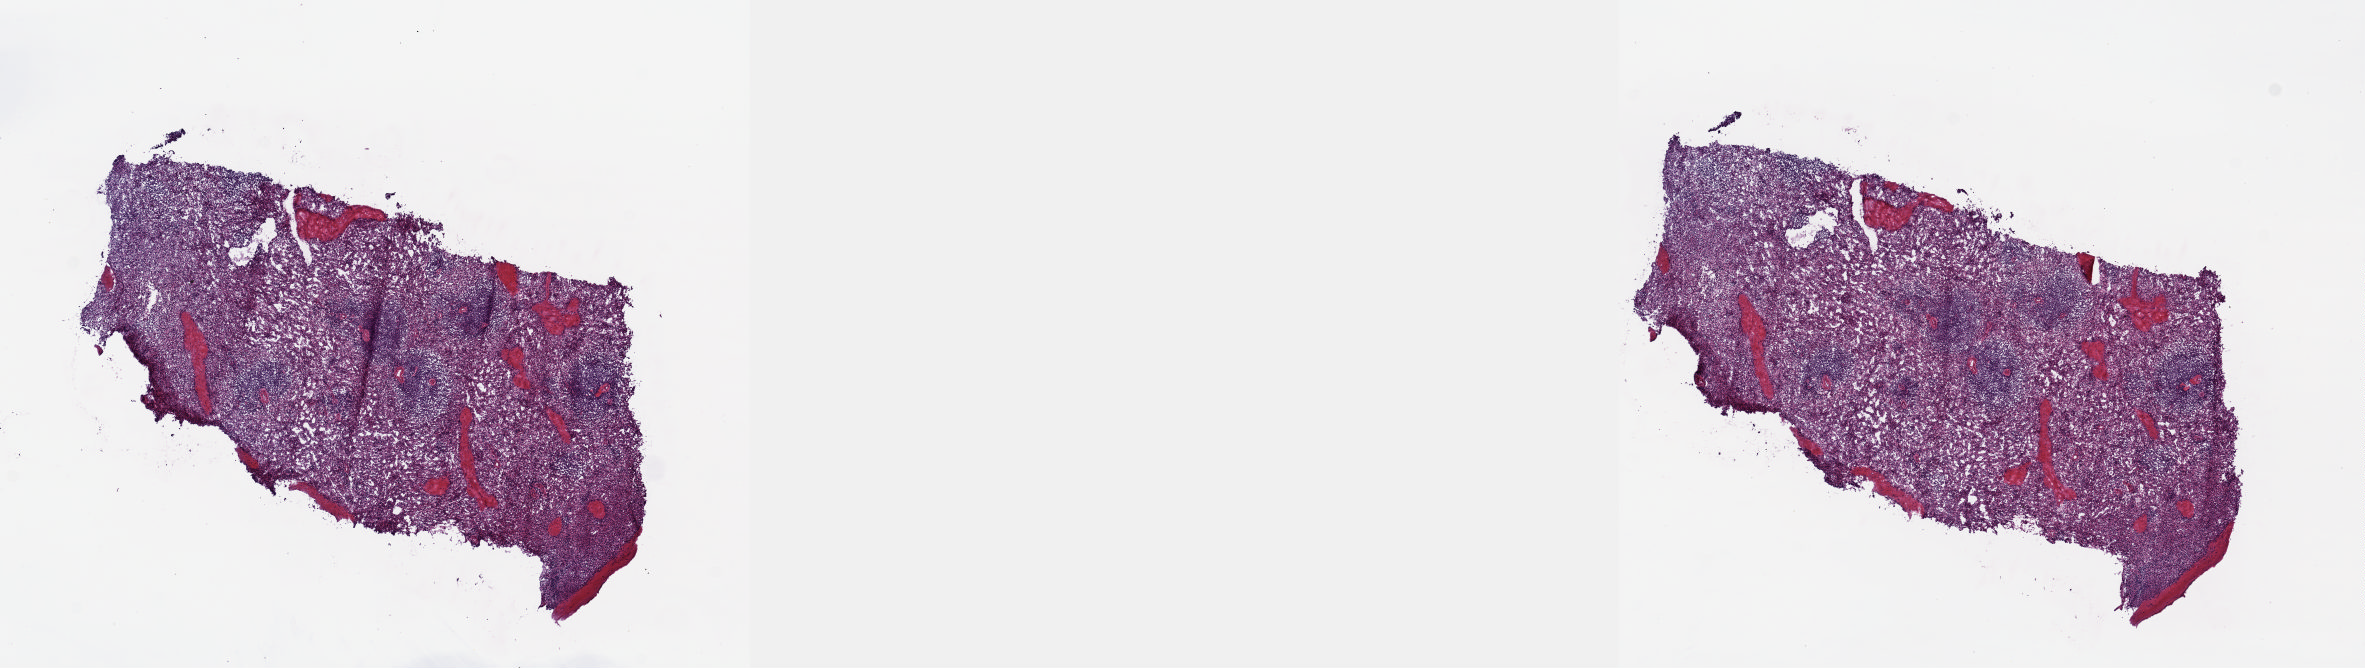
Digitized H&E tissue section (whole slide) — shown as a low-resolution overview of the whole scanned area (about 19.1 x 5.4 mm, slide scanned at 20x). Frozen section from the top of the tissue portion. Sample: solid tissue normal (non-tumour tissue), pancreas. Male, age 85 years at initial diagnosis. Composition of this section per pathologist review: tumour cells 0%, tumour nuclei 0%, normal cells 0%, stromal cells 100%, necrosis 0%. Infiltration values recorded for this section: lymphocyte infiltration 50%, monocyte infiltration 40%, neutrophil infiltration 5%.
This section: solid tissue normal (non-tumour) sample from the same patient. Patient diagnosis: Infiltrating duct carcinoma, NOS (tail of pancreas).